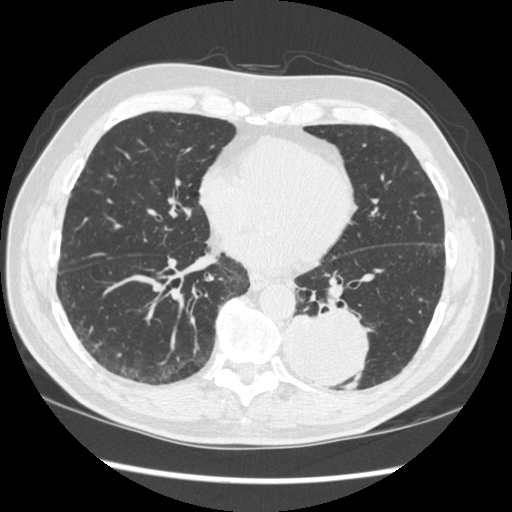
Low-dose screening chest CT, one axial slice. Slice 131 of 348 in the series (ordered by position). Lung window (W 1500 / L -600 HU). 512 × 512 image matrix, field of view 360 × 360 mm.
Annotated regions visible in this slice (manually delineated by an expert):
- lesion 1 (tumor, lower lobe of left lung): box from (x=284, y=311) to (x=368, y=389) px